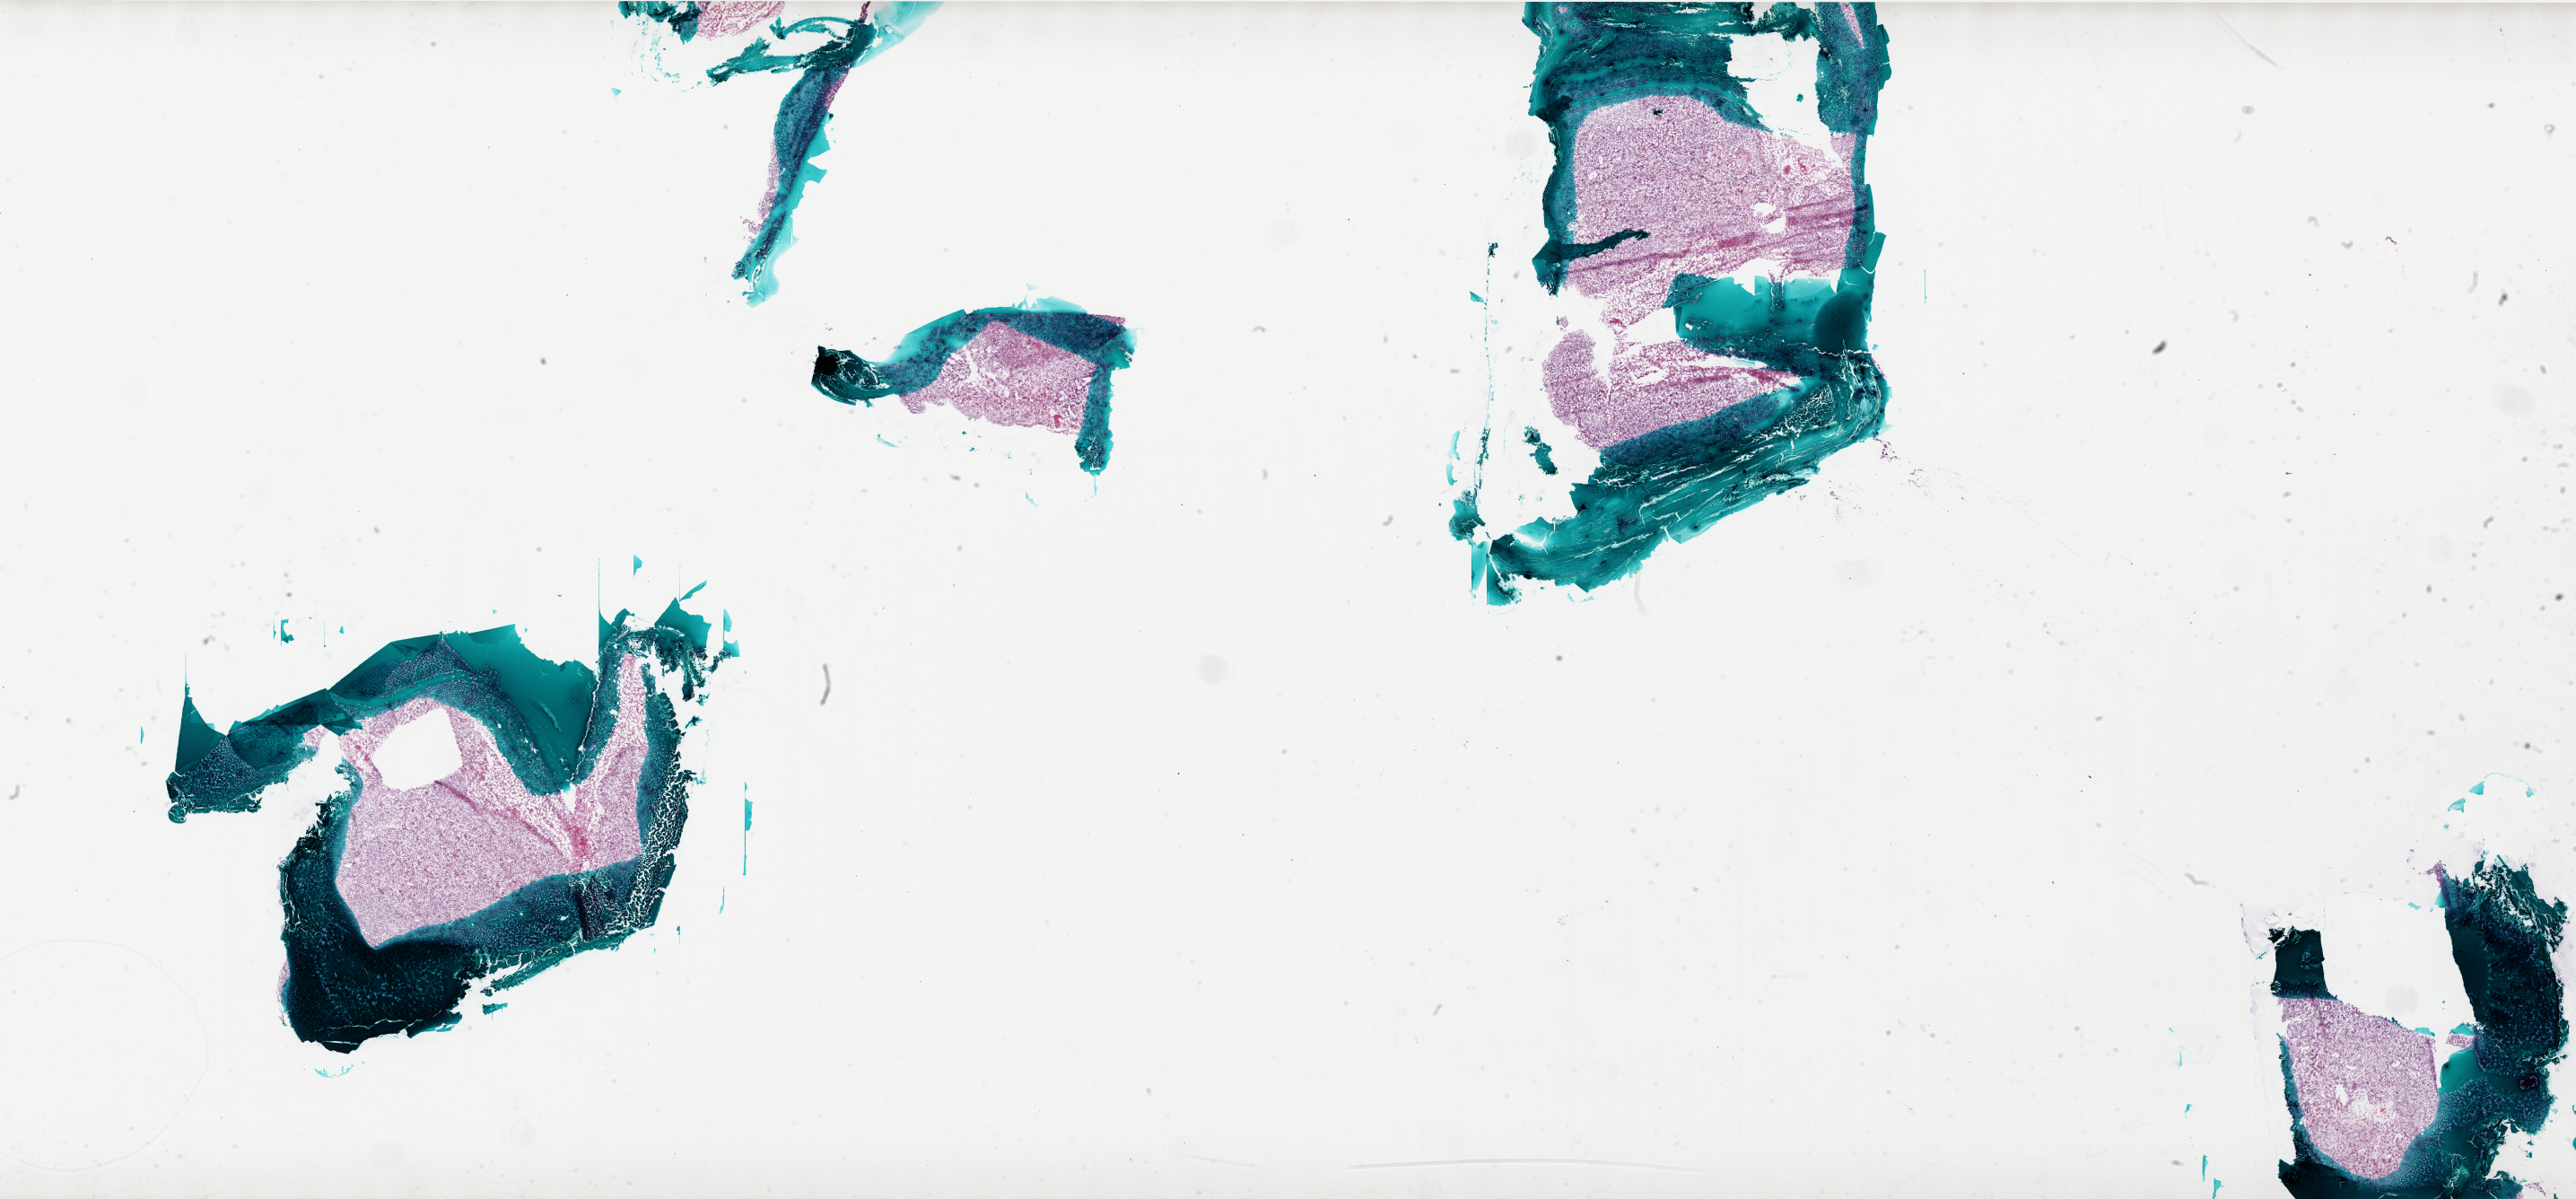
Digitized Hematoxylin and eosin (H&E) stained tissue section (whole slide), low-resolution overview of the scanned area, about 46.0 x 21.4 mm (slide scanned at 20x); frozen section from the bottom of the tissue portion; brain, primary tumour sample. Male patient; age at initial diagnosis 42 years. Composition of this section per pathologist review: tumour cells 80%, tumour nuclei 100%, normal cells 0%, stromal cells 0%, necrosis 20%.
• histologic diagnosis: Glioblastoma